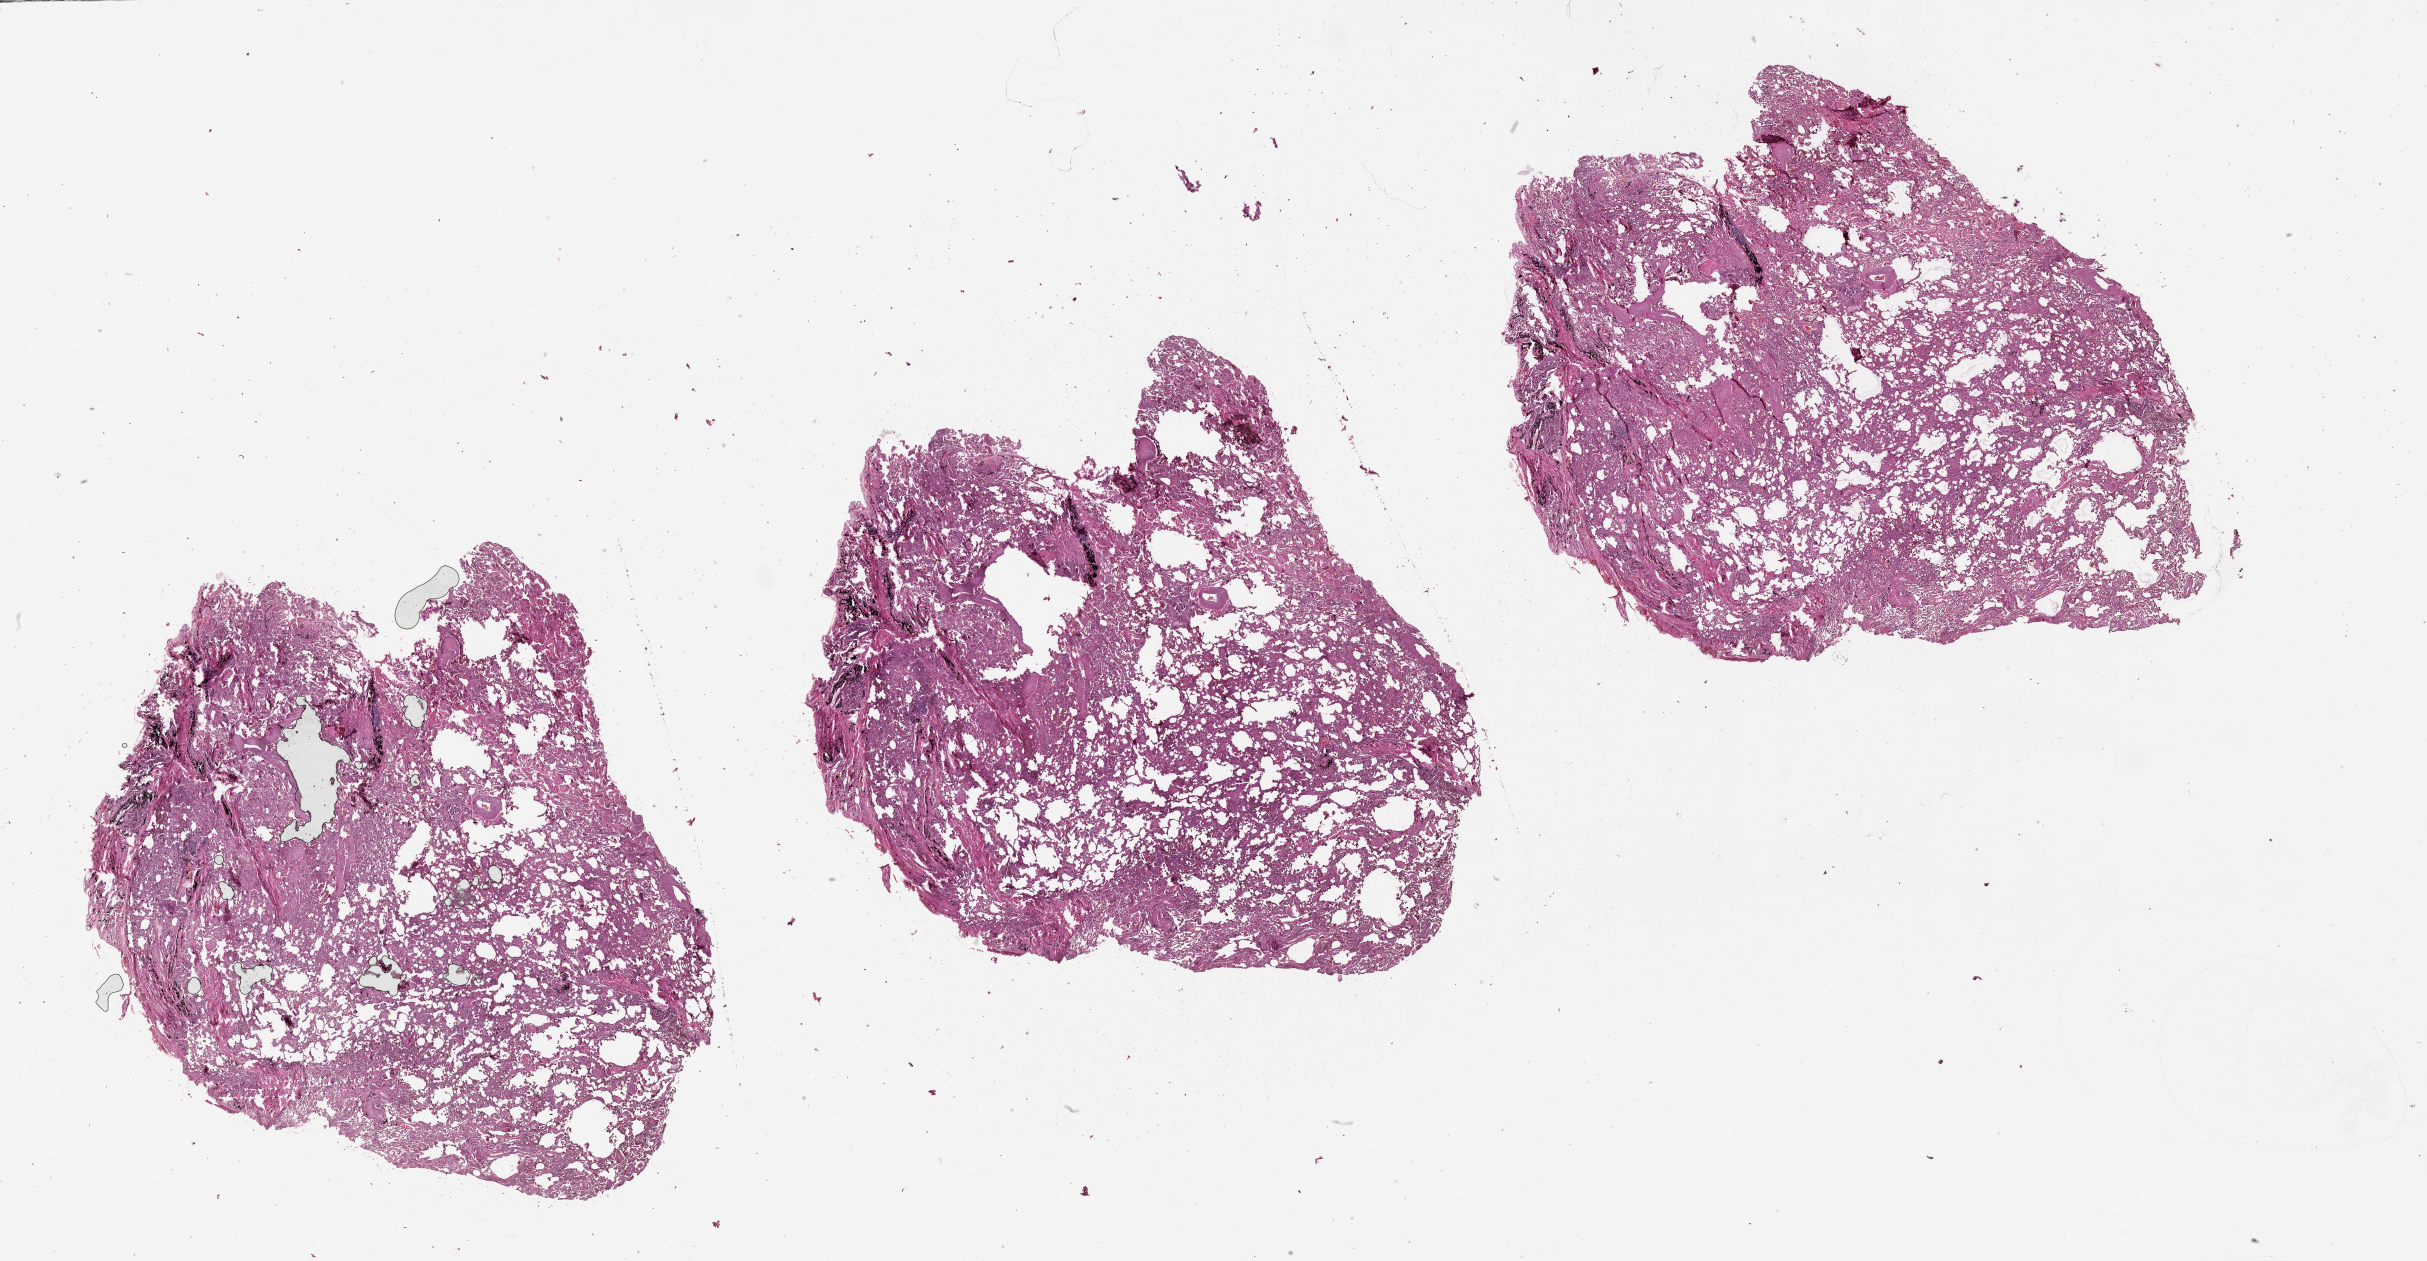
Whole-slide histology image, H&E — whole scanned area (about 39.1 x 20.3 mm, from a 20x scan) shown as a low-resolution overview; lung, normal (non-tumour) tissue. Patient: male, age 63 years.
This section: normal (non-tumour) tissue from the same patient. Patient diagnosis (cohort enrolment): squamous cell carcinoma (lung).